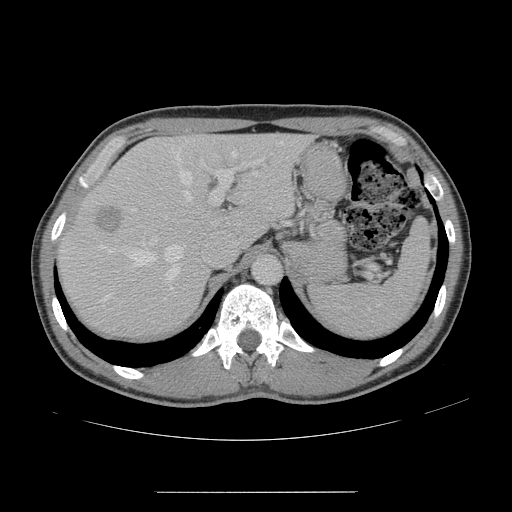
Contrast-enhanced abdominal CT, one axial slice; position 109 of 178 along the scan axis; 120 kVp; intravenous contrast given; soft-tissue window (W 400 / L 40 HU); 2.5 mm slice thickness; 512 × 512 image matrix. Male patient, age 53 years. Case-level facts recorded for this patient, not image findings: diagnosis: colorectal cancer liver metastases, imaged before liver resection; multiple liver metastases: yes; largest metastasis: 2.4 cm; chemotherapy before resection: yes.
Annotated regions visible in this slice (manually delineated by an expert):
- hepatic veins: bounding box <103,141,283,300> (left, top, right, bottom; pixels)
- liver: <59,135,306,337>
- planned liver remnant (the part of the liver to remain after resection): <147,135,306,243>
- portal vein (with intrahepatic branches): <132,158,264,212>
- liver metastasis: <92,205,127,235>